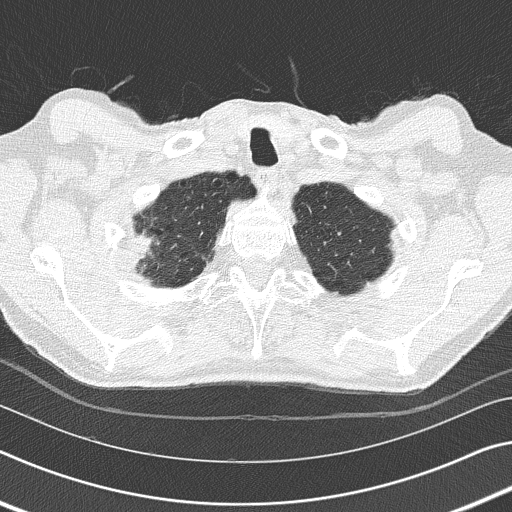
Low-dose screening chest CT, one axial slice. Reconstruction kernel B50f. Lung window (W 1500 / L -600 HU). 2 mm slice thickness. 512 × 512 image matrix.
Structures marked on this image (outlined manually by an expert reader):
- lesion 1 (tumor, middle lobe of right lung): box from (x=135, y=231) to (x=156, y=268) px